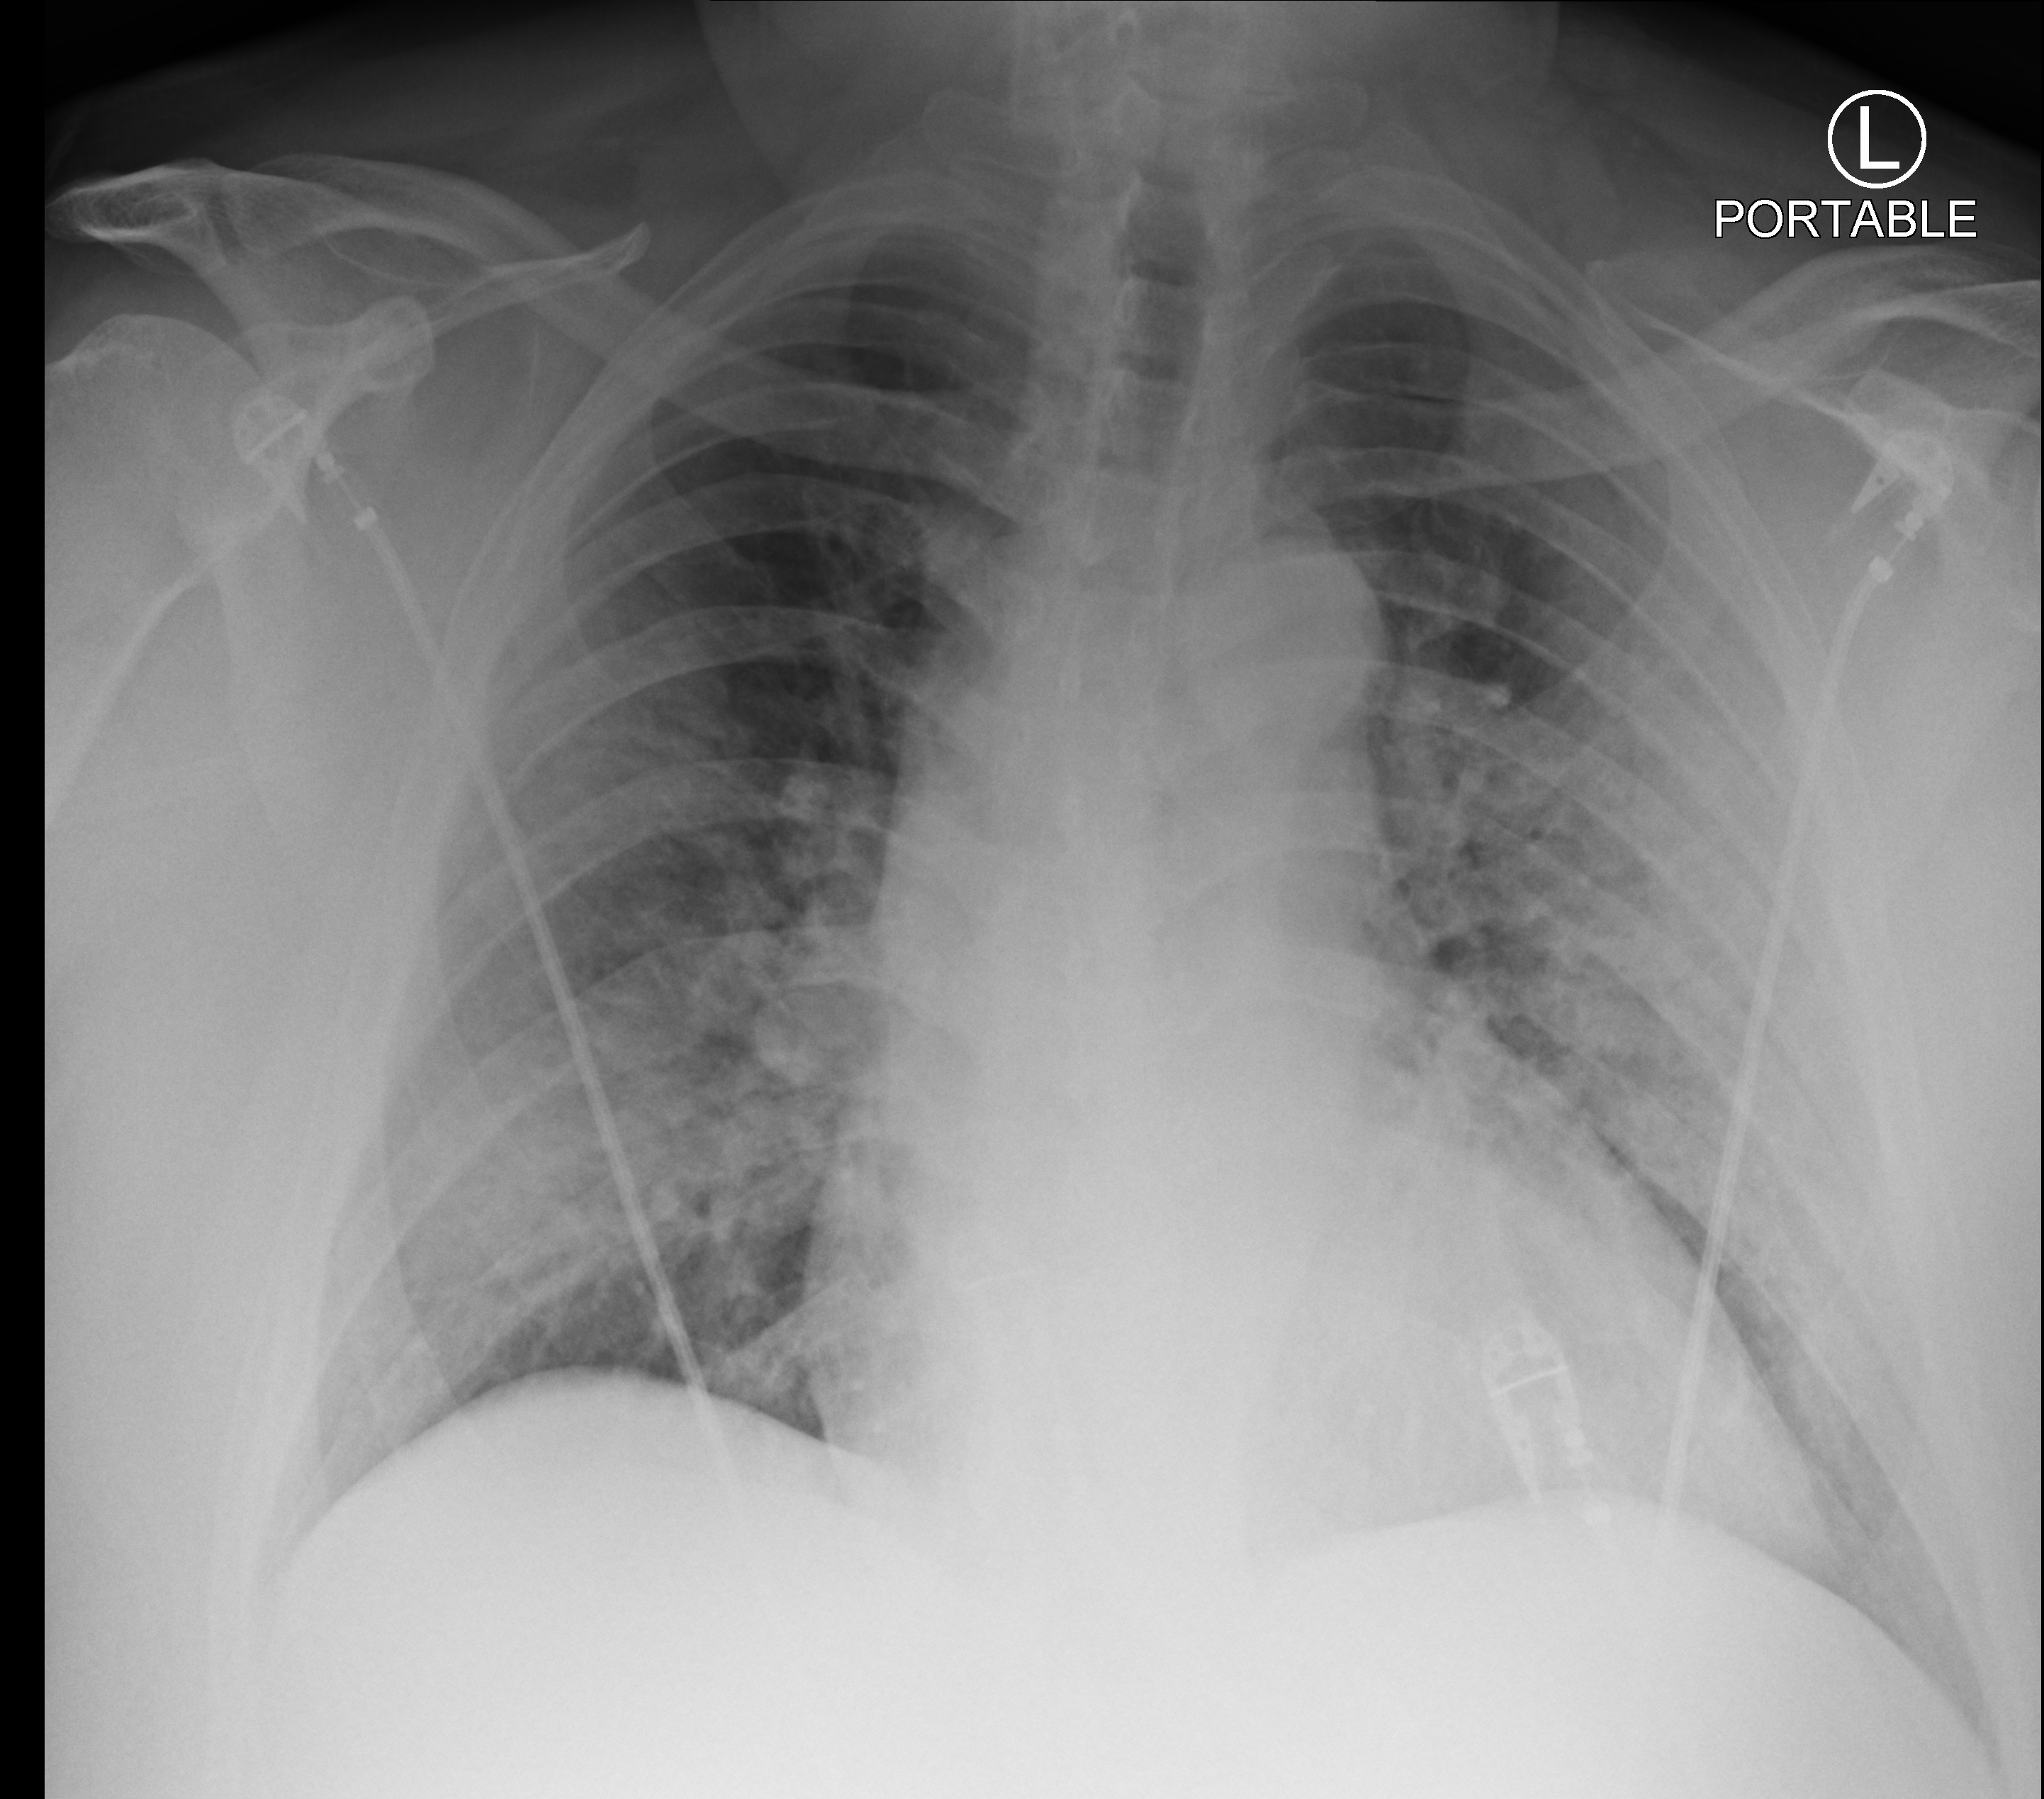
Bedside chest radiograph (computed radiography), anteroposterior (AP) projection. Patient hospitalised with COVID-19; male, aged 60–74 years.
Hospital-stay facts (about this admission, not read from this image; timing relative to this image not recorded): admitted to intensive care during this hospital stay: yes; hypertension (admission record): yes.